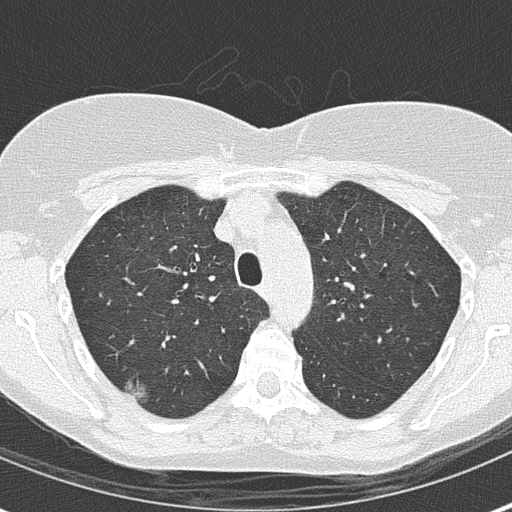
Chest CT (low-dose screening protocol), one axial image. Baseline screening round. Lung window (W 1500 / L -600 HU). Lung (sharp) reconstruction kernel (B50f). Female participant, aged 56 years at enrolment.
Expert reader's lesion annotation, bounding box [x1, y1, x2, y2] px = [110, 361, 162, 413]. The screening reader recorded 2 non-calcified nodules or masses ≥4 mm on this exam (right upper lobe, left upper lobe); which of them this box marks is not recorded.